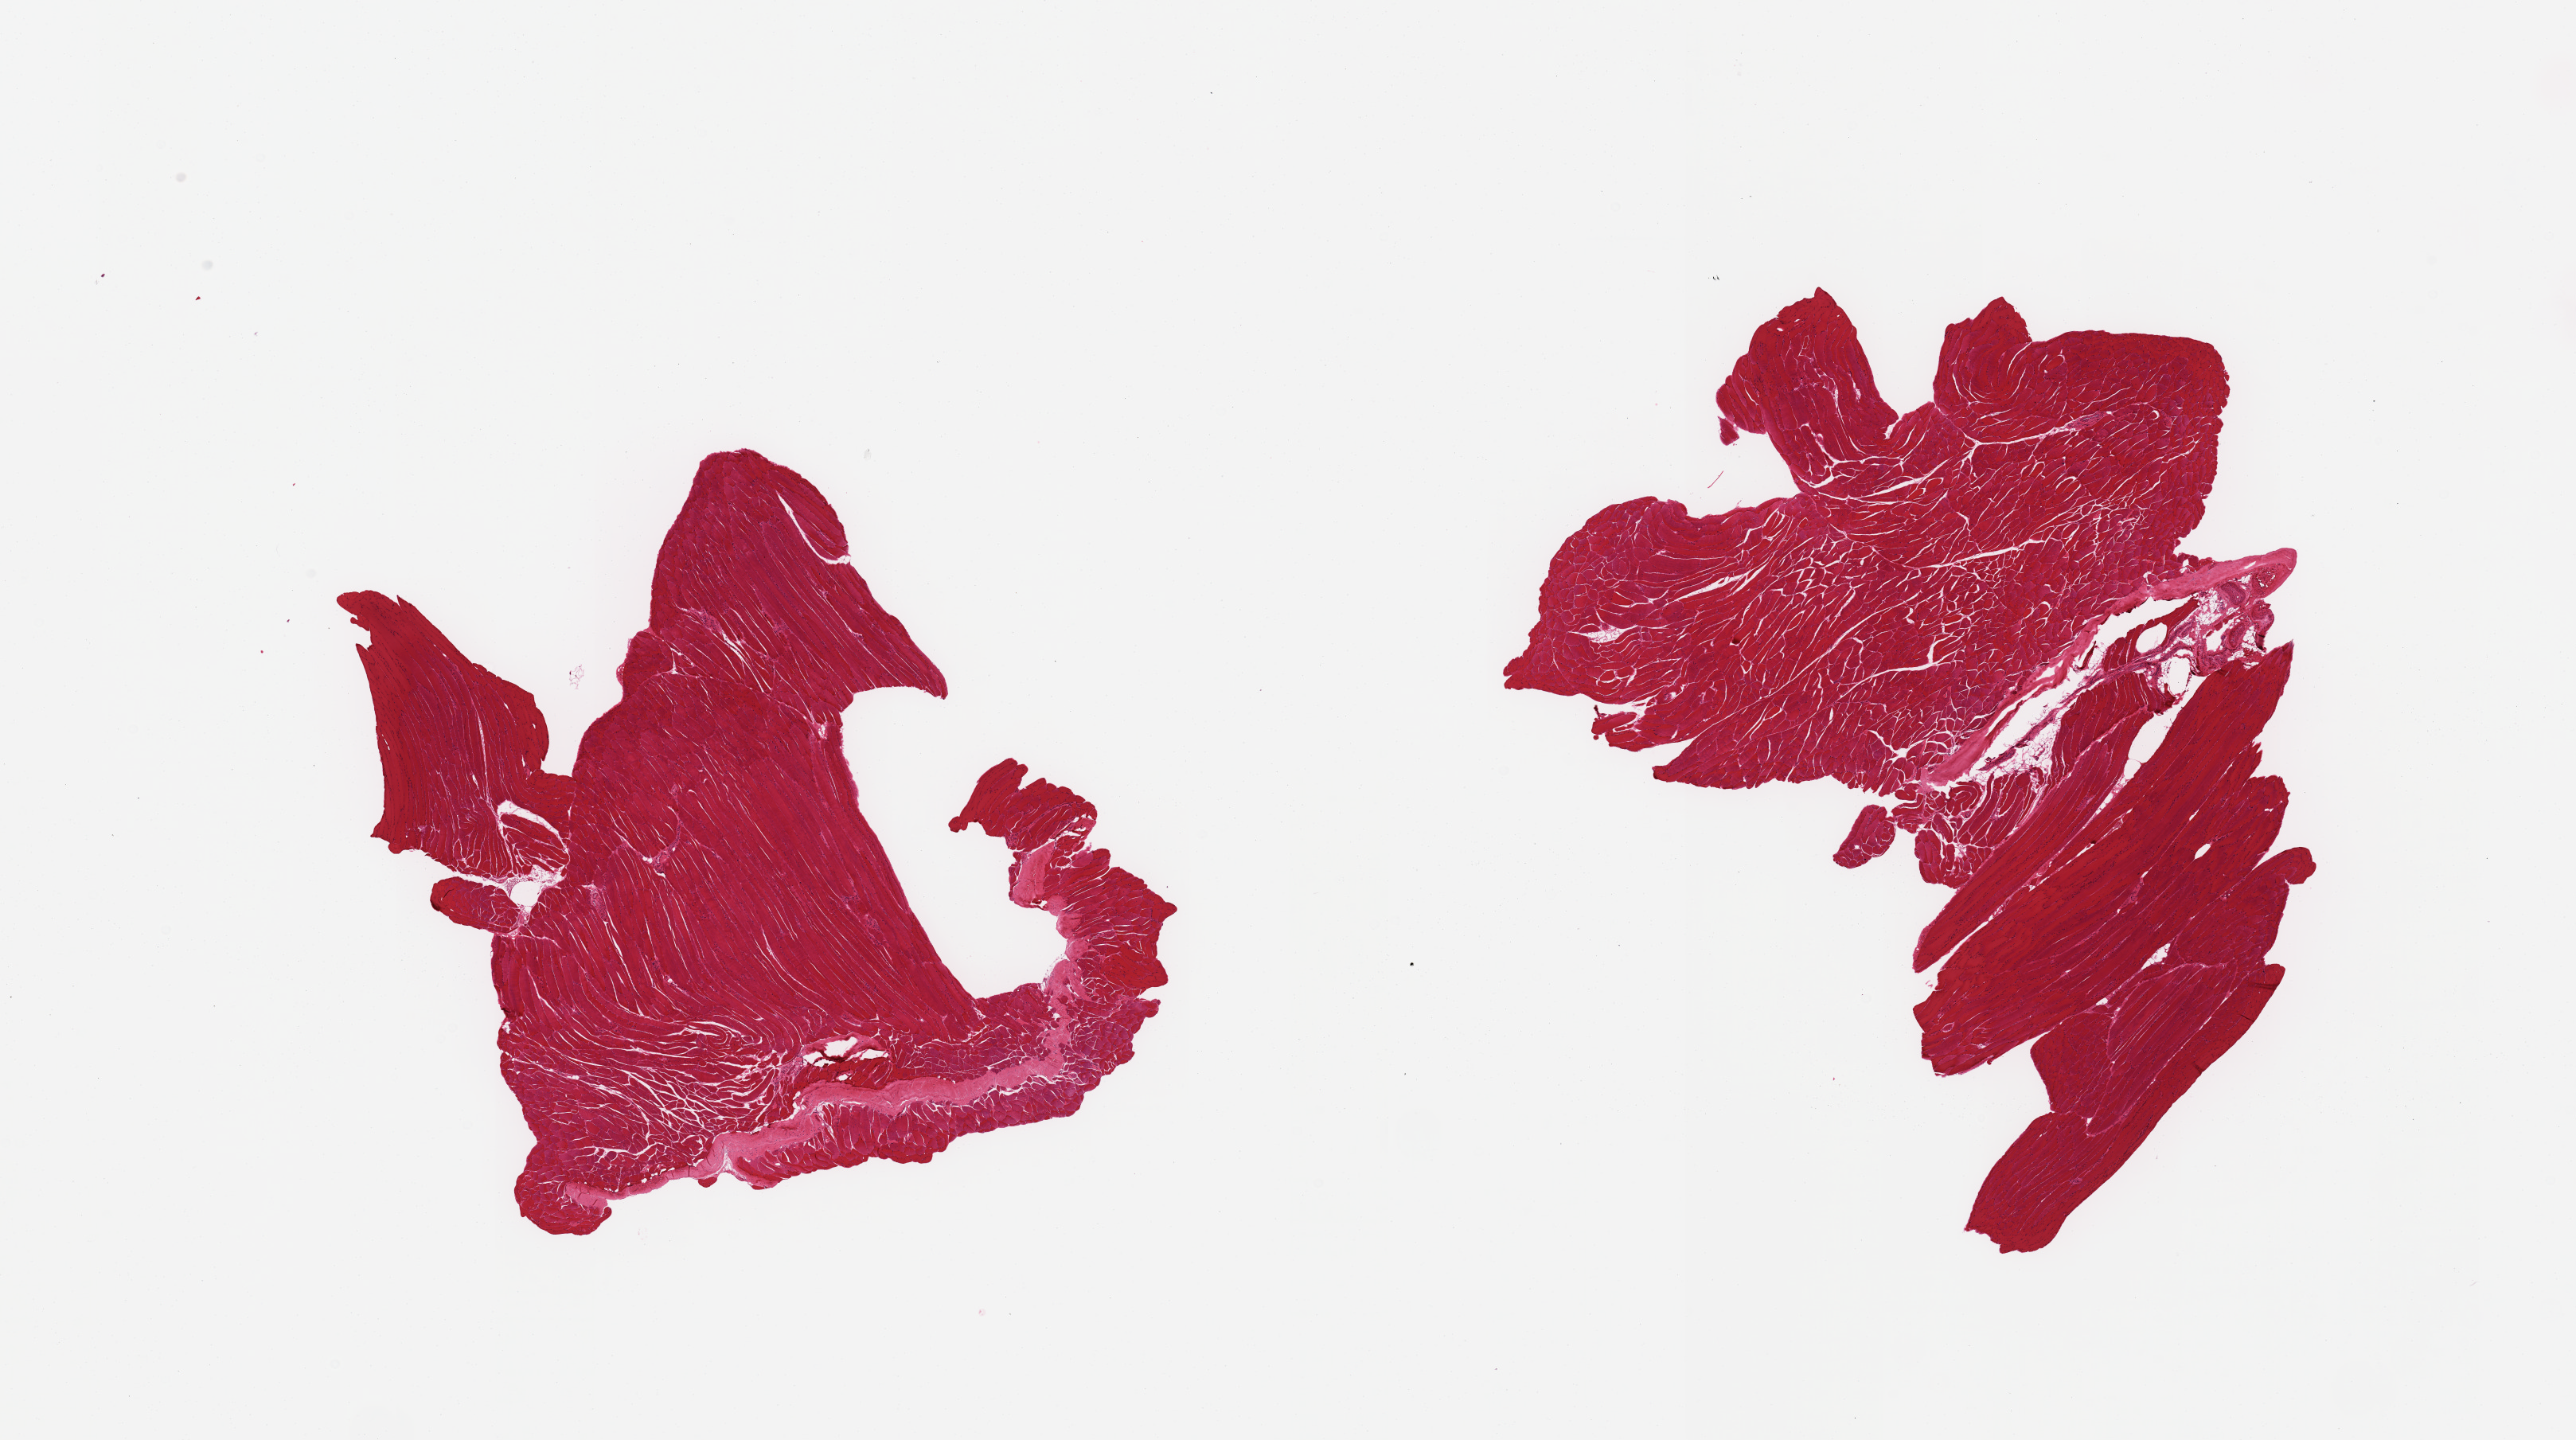
Digitized H&E-stained section, brightfield — low-resolution overview of the scanned area, about 25.6 x 14.3 mm (acquisition: 20x scan). PAXgene-fixed paraffin-embedded (PFPE) section. Section of skeletal muscle (target tissue). Tissue donor sample. Donor sex: female.
Reviewer comment on this tissue sample: 2 pieces, ~5% tendon/vascular elements.